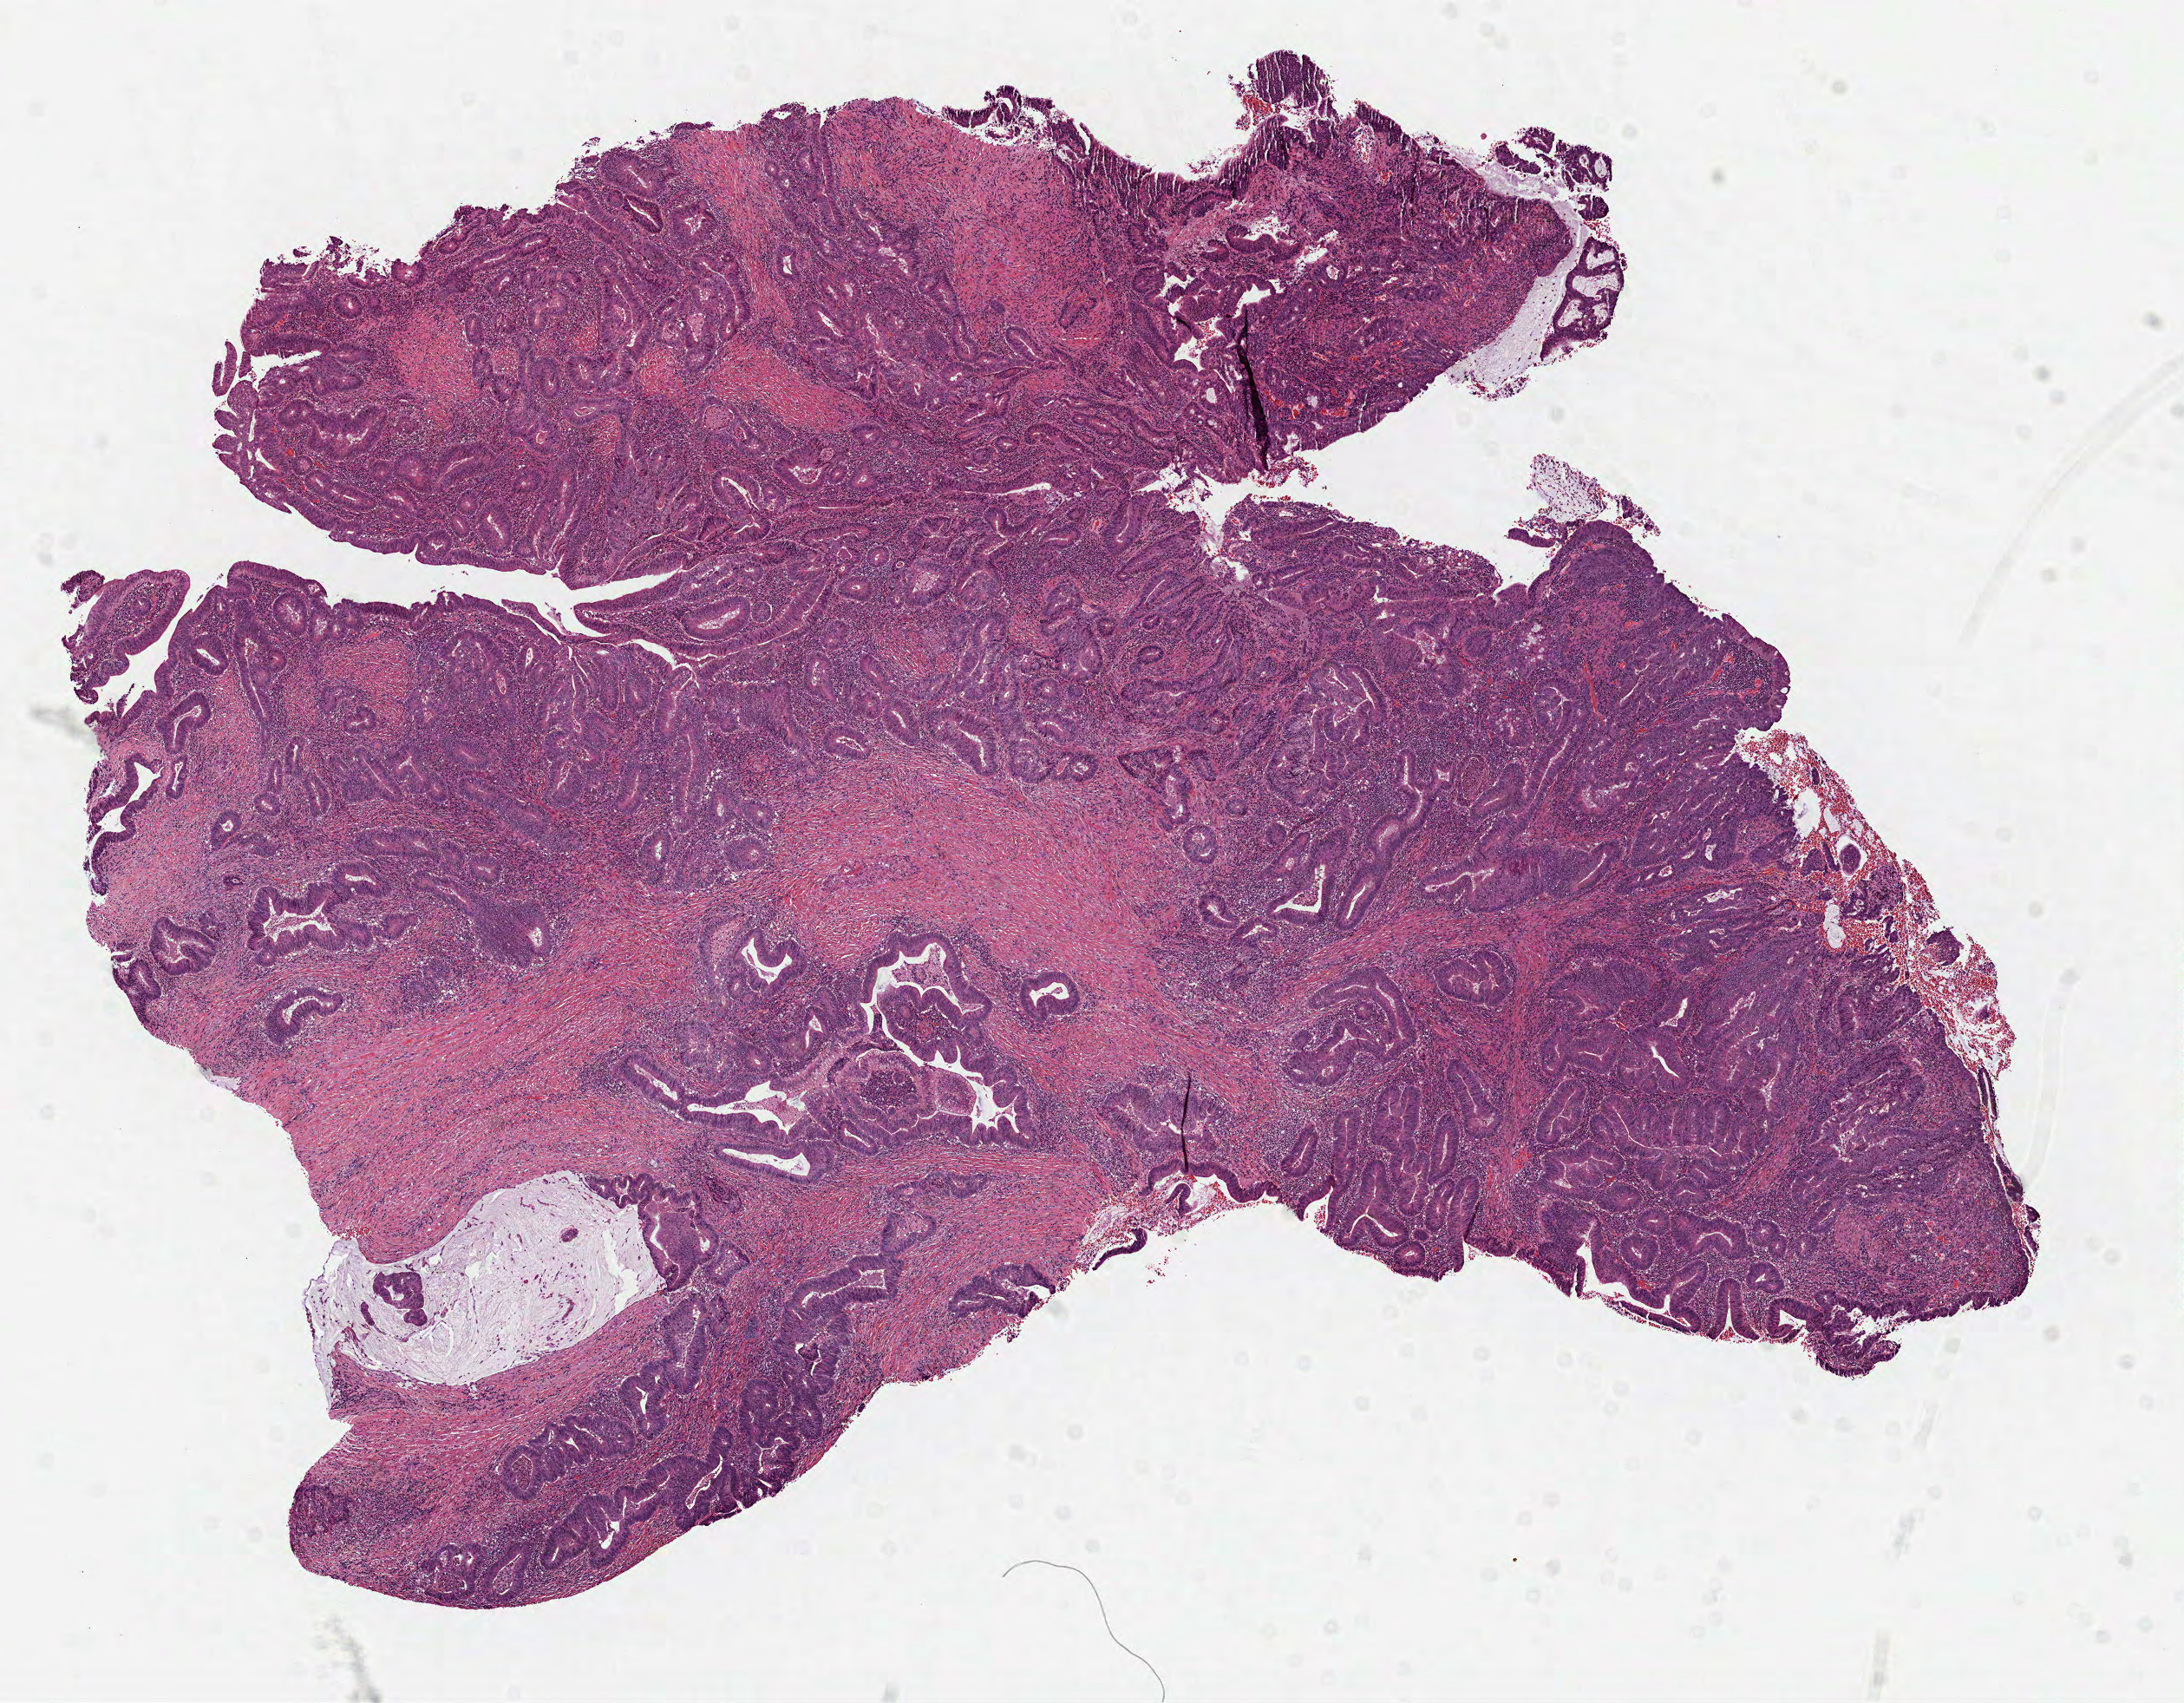
Digitized H&E tissue section (whole slide) — low-resolution overview of the scanned area, about 10.2 x 7.9 mm. FFPE section. Sample: primary tumour, colon. Male patient; age at initial diagnosis 31 years.
- diagnosis: Adenocarcinoma, NOS
- AJCC pathologic stage: IIA (7th edition)